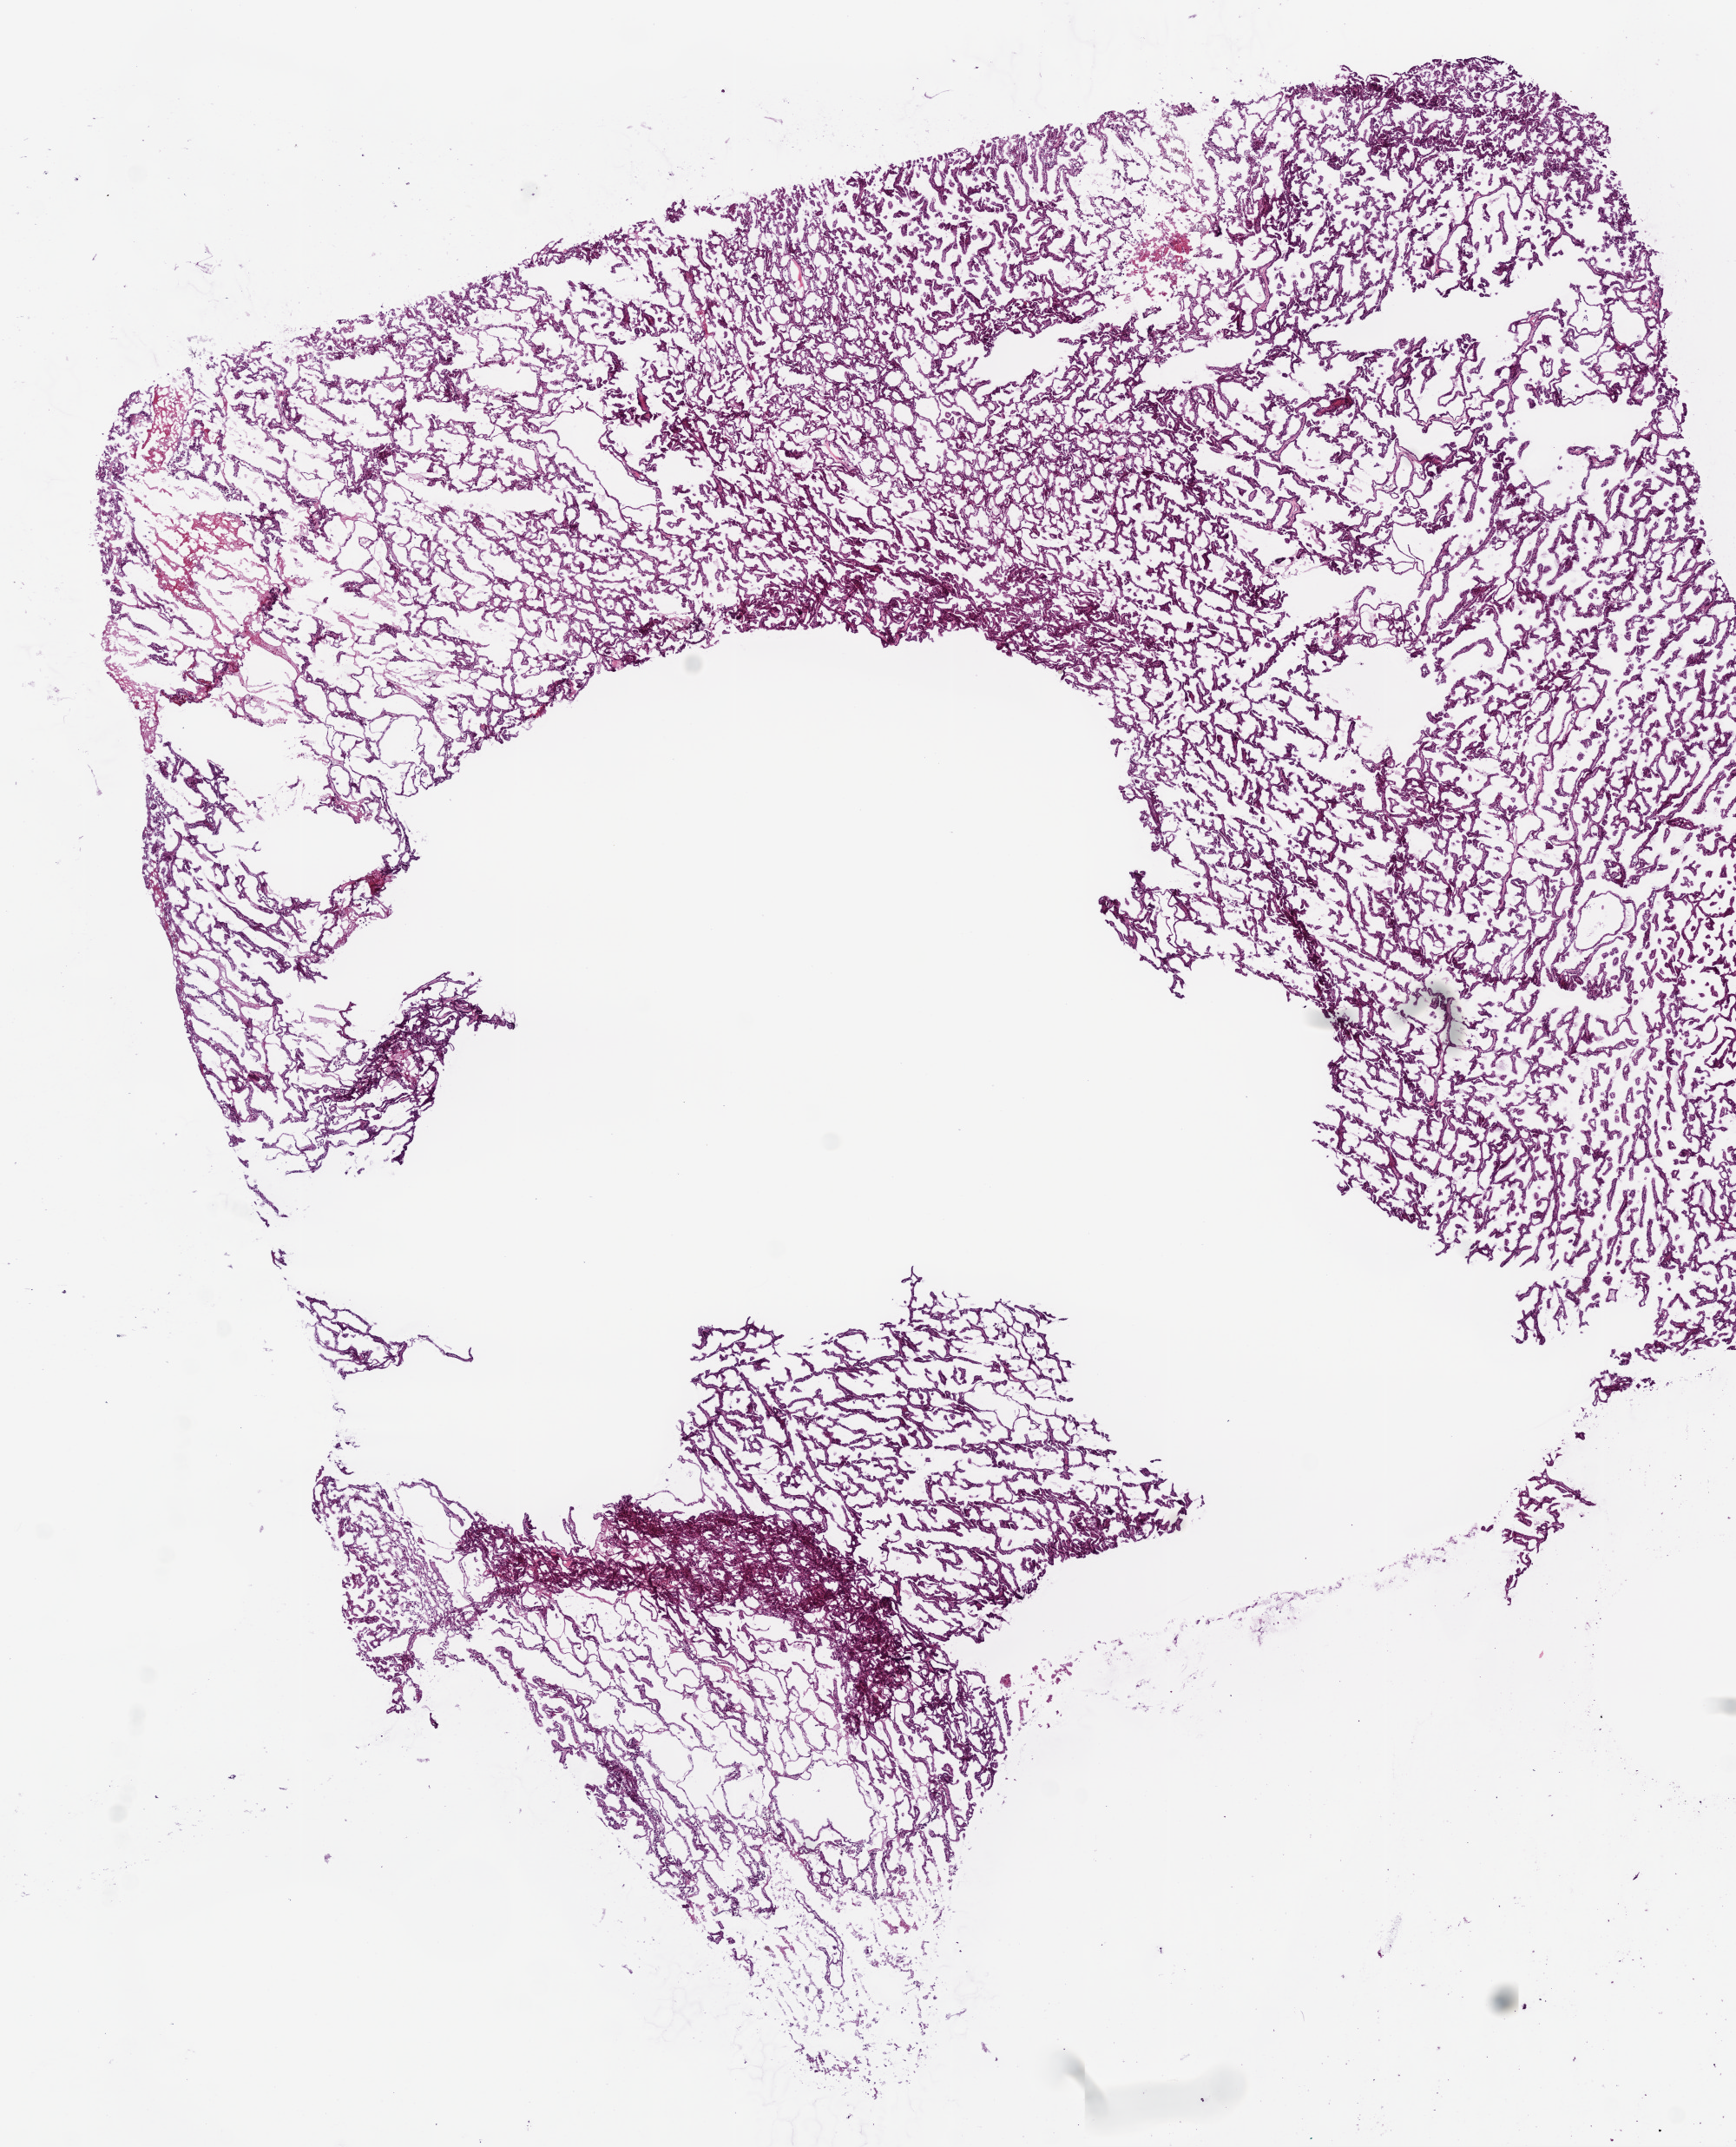
Whole-slide histology image, H&E-stained — low-resolution overview of the scanned area, about 8.0 x 9.9 mm, frozen section from the bottom of the tissue portion, sample: primary tumour, kidney. Male, age 74 years at initial diagnosis.
Diagnosis: Papillary adenocarcinoma, NOS.